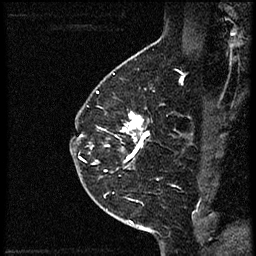
Breast MRI (dynamic contrast-enhanced), one sagittal slice. Position 41 of 56 along the scan axis. Dynamic contrast-enhanced study with each time point stored as its own series, time point 2 of 4 at this slice position (early post-contrast, ordered by acquisition time). 1.5 T. TE 4.2 ms, TR 18.9 ms. 2 mm slice thickness. 256 × 256 image matrix. Female patient. Case-level facts recorded for this patient, not image findings: setting: breast cancer imaged before/during neoadjuvant chemotherapy; receptor status: HER2-positive.
Outlined on this slice (semi-automatically segmented with operator editing):
- analysis volume of interest (the breast-tissue region the enhancement analysis was run in; not a lesion): box from (x=78, y=107) to (x=160, y=189) px
- tumour enhancement mask (voxels above the 100 % enhancement threshold inside the analysis volume of interest): (x=91, y=111)–(x=150, y=171)